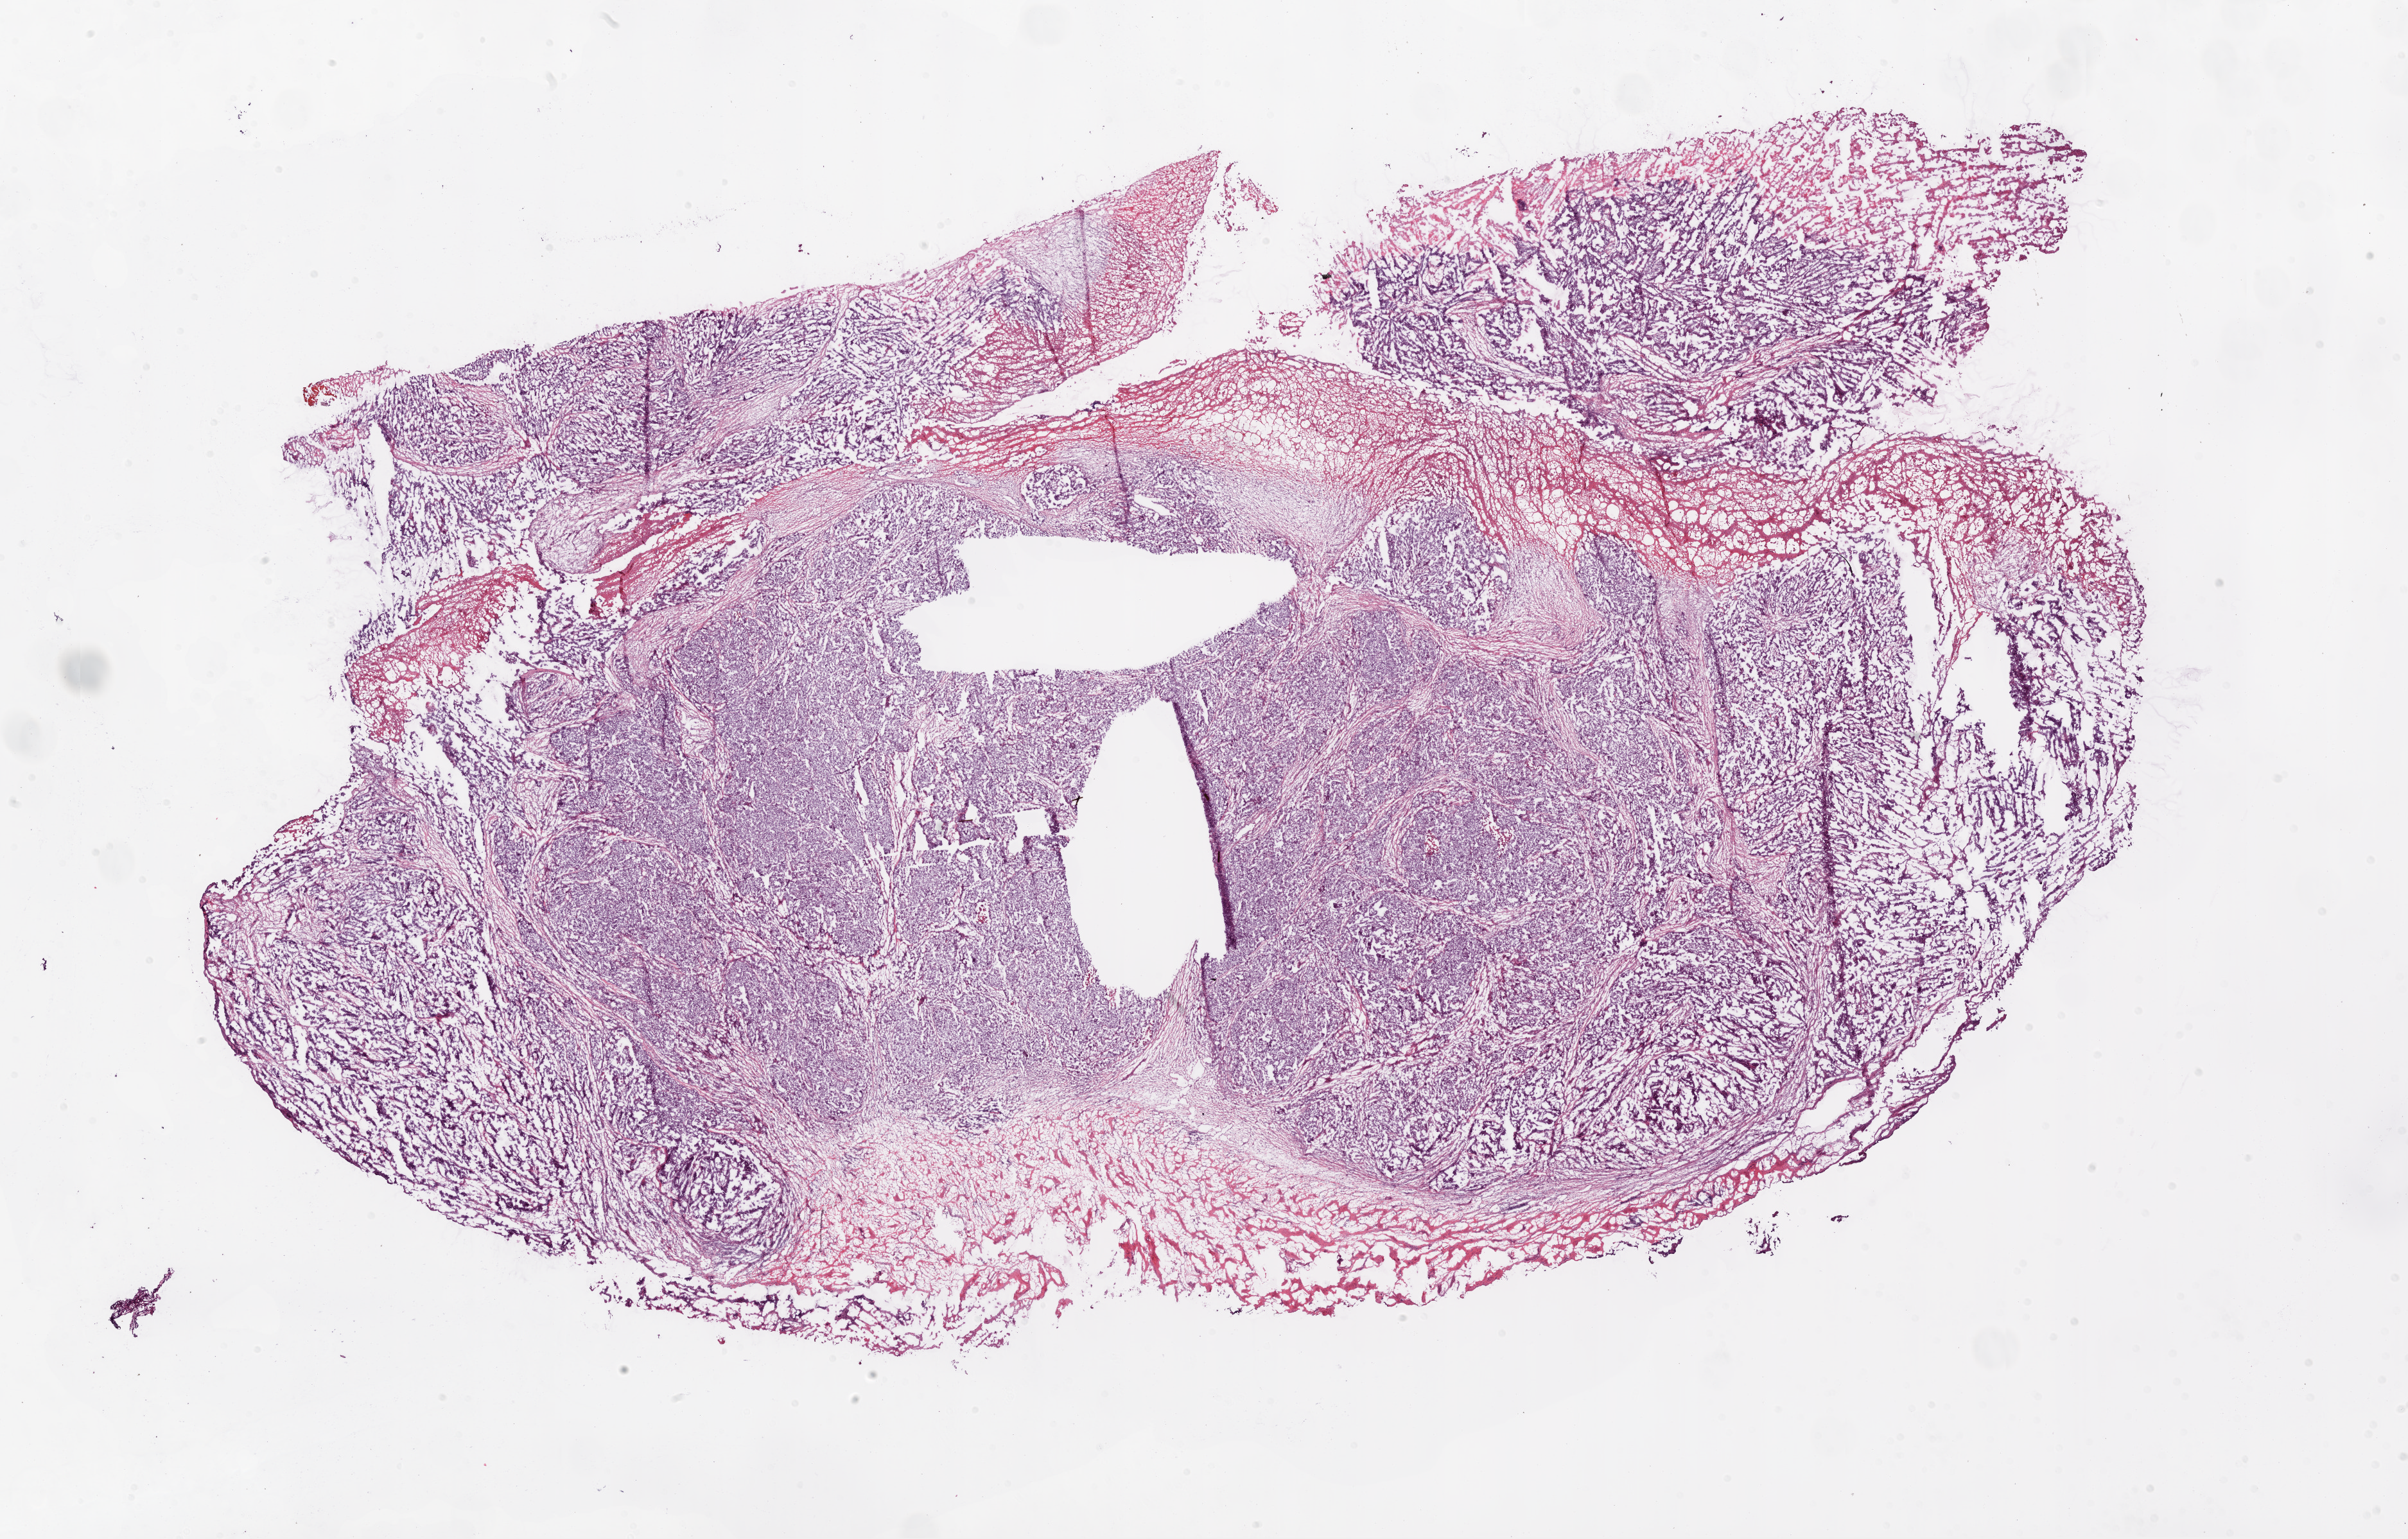
H&E-stained whole-slide image — shown as a low-resolution overview of the whole scanned area (about 30.1 x 19.2 mm, slide scanned at 20x), frozen section, primary tumour sample from the ovary. Patient: female, age at initial diagnosis 51 years. Histologic grade: G3 (poorly differentiated). Slide review estimates, as recorded: tumour cells 85%, tumour nuclei 70%, normal cells 0%, stromal cells 10%, necrosis 5%. Inflammatory infiltration, as recorded: lymphocyte infiltration 20%, monocyte infiltration 0%, neutrophil infiltration 0%.
* laterality: bilateral
* FIGO stage: IV
* histologic diagnosis: Serous cystadenocarcinoma, NOS